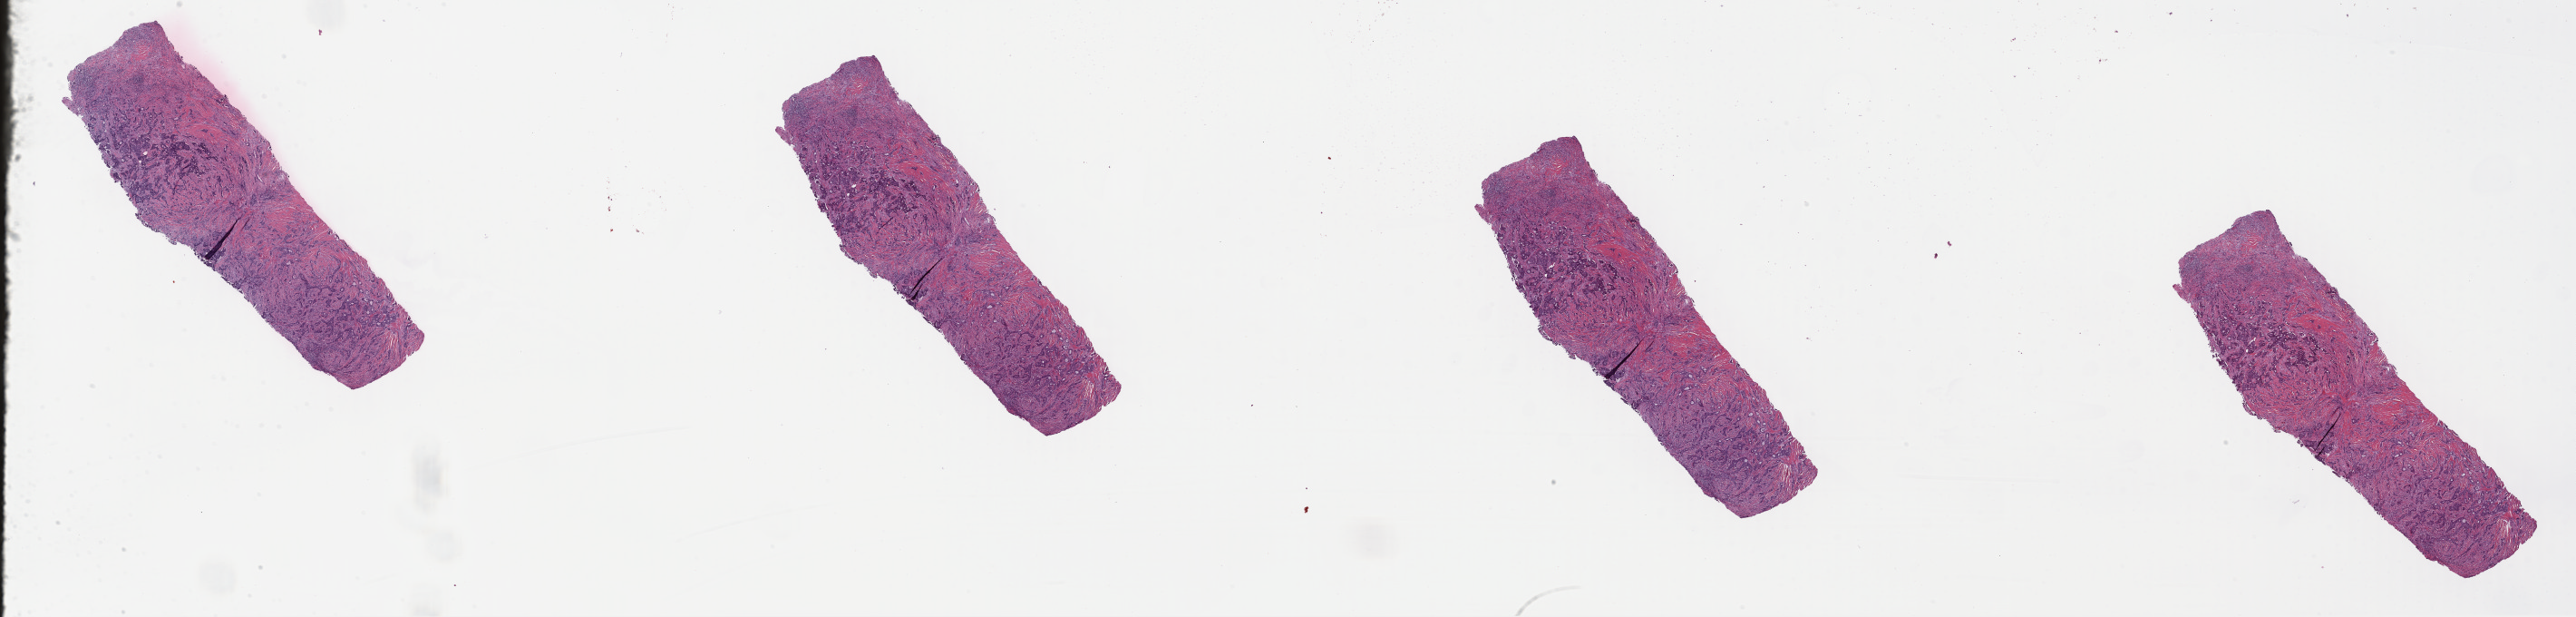
H&E whole-slide image, shown as a low-resolution overview of the whole scanned area (about 44.7 x 10.7 mm); FFPE section; breast, primary tumour sample. Female patient; age at initial diagnosis 84 years.
- pathologic diagnosis: Infiltrating duct carcinoma, NOS
- AJCC pathologic stage: IIA (7th edition)
- lymph nodes positive (case pathology): 0 of 8 examined
- laterality: left
- TNM: T2 N0 M0